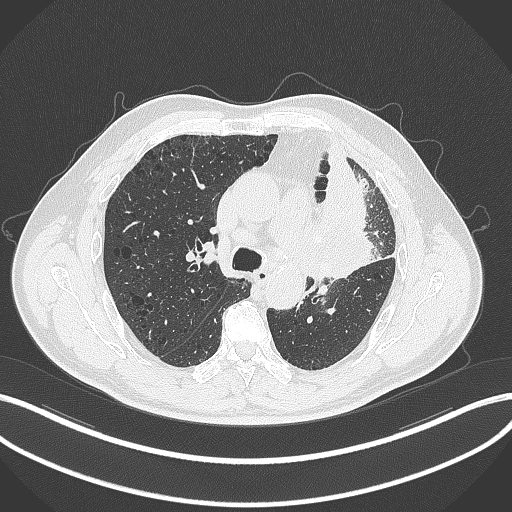
Chest CT, one axial slice; slice 200 of 297 in the series (ordered by position); 120 kVp; lung window (W 1500 / L -600 HU); 1 mm slice thickness; 512 × 512 image matrix, field of view 400 × 400 mm. Patient: male, 68 years. From the clinical record (not read from this slice): clinical TNM (as recorded): T3 N3 M1.
Structures marked on this image (rectangle marked by the reading radiologist):
- lung tumour (recorded histology: adenocarcinoma): bounding box <315,160,381,284> (left, top, right, bottom; pixels)